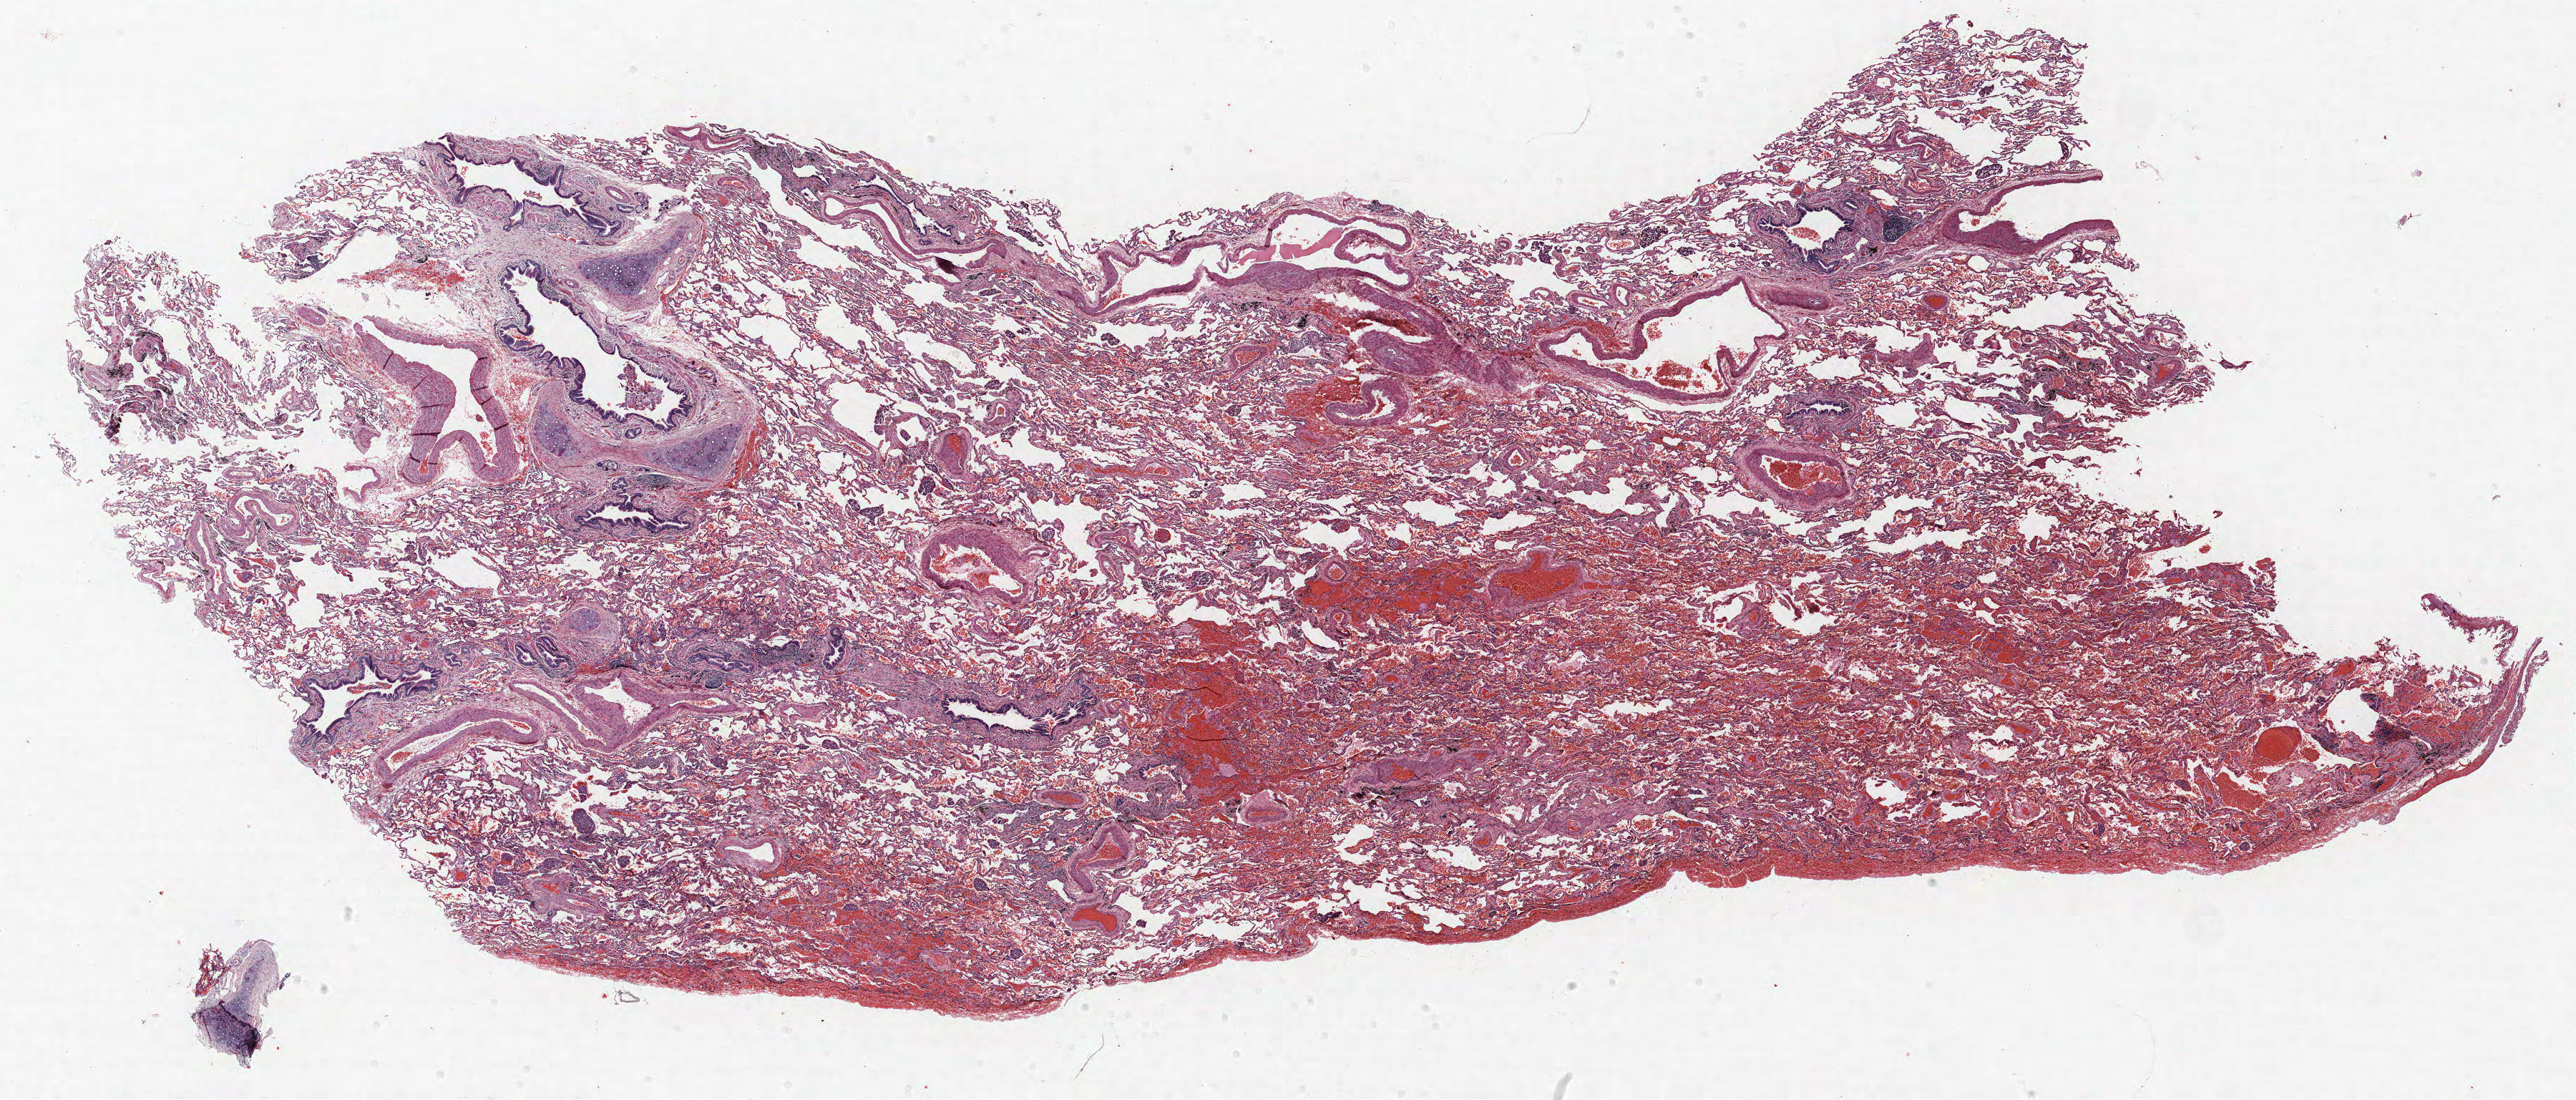
H&E-stained whole-slide image, a low-resolution overview of the entire scanned area, about 28.8 x 12.3 mm (slide scanned at 40x). FFPE section. Lung. Male, age 69 at enrolment. Current smoker at enrolment. Grade: moderately differentiated (G2).
* ICD-O-3 topography: upper lobe of lung (C34.1)
* primary tumour location (clinical record): left upper lobe
* participant's lung-cancer diagnosis: Adenocarcinoma with mixed subtypes
* tumour size (pathology): 10 mm
* stage (AJCC 6th edition): IA